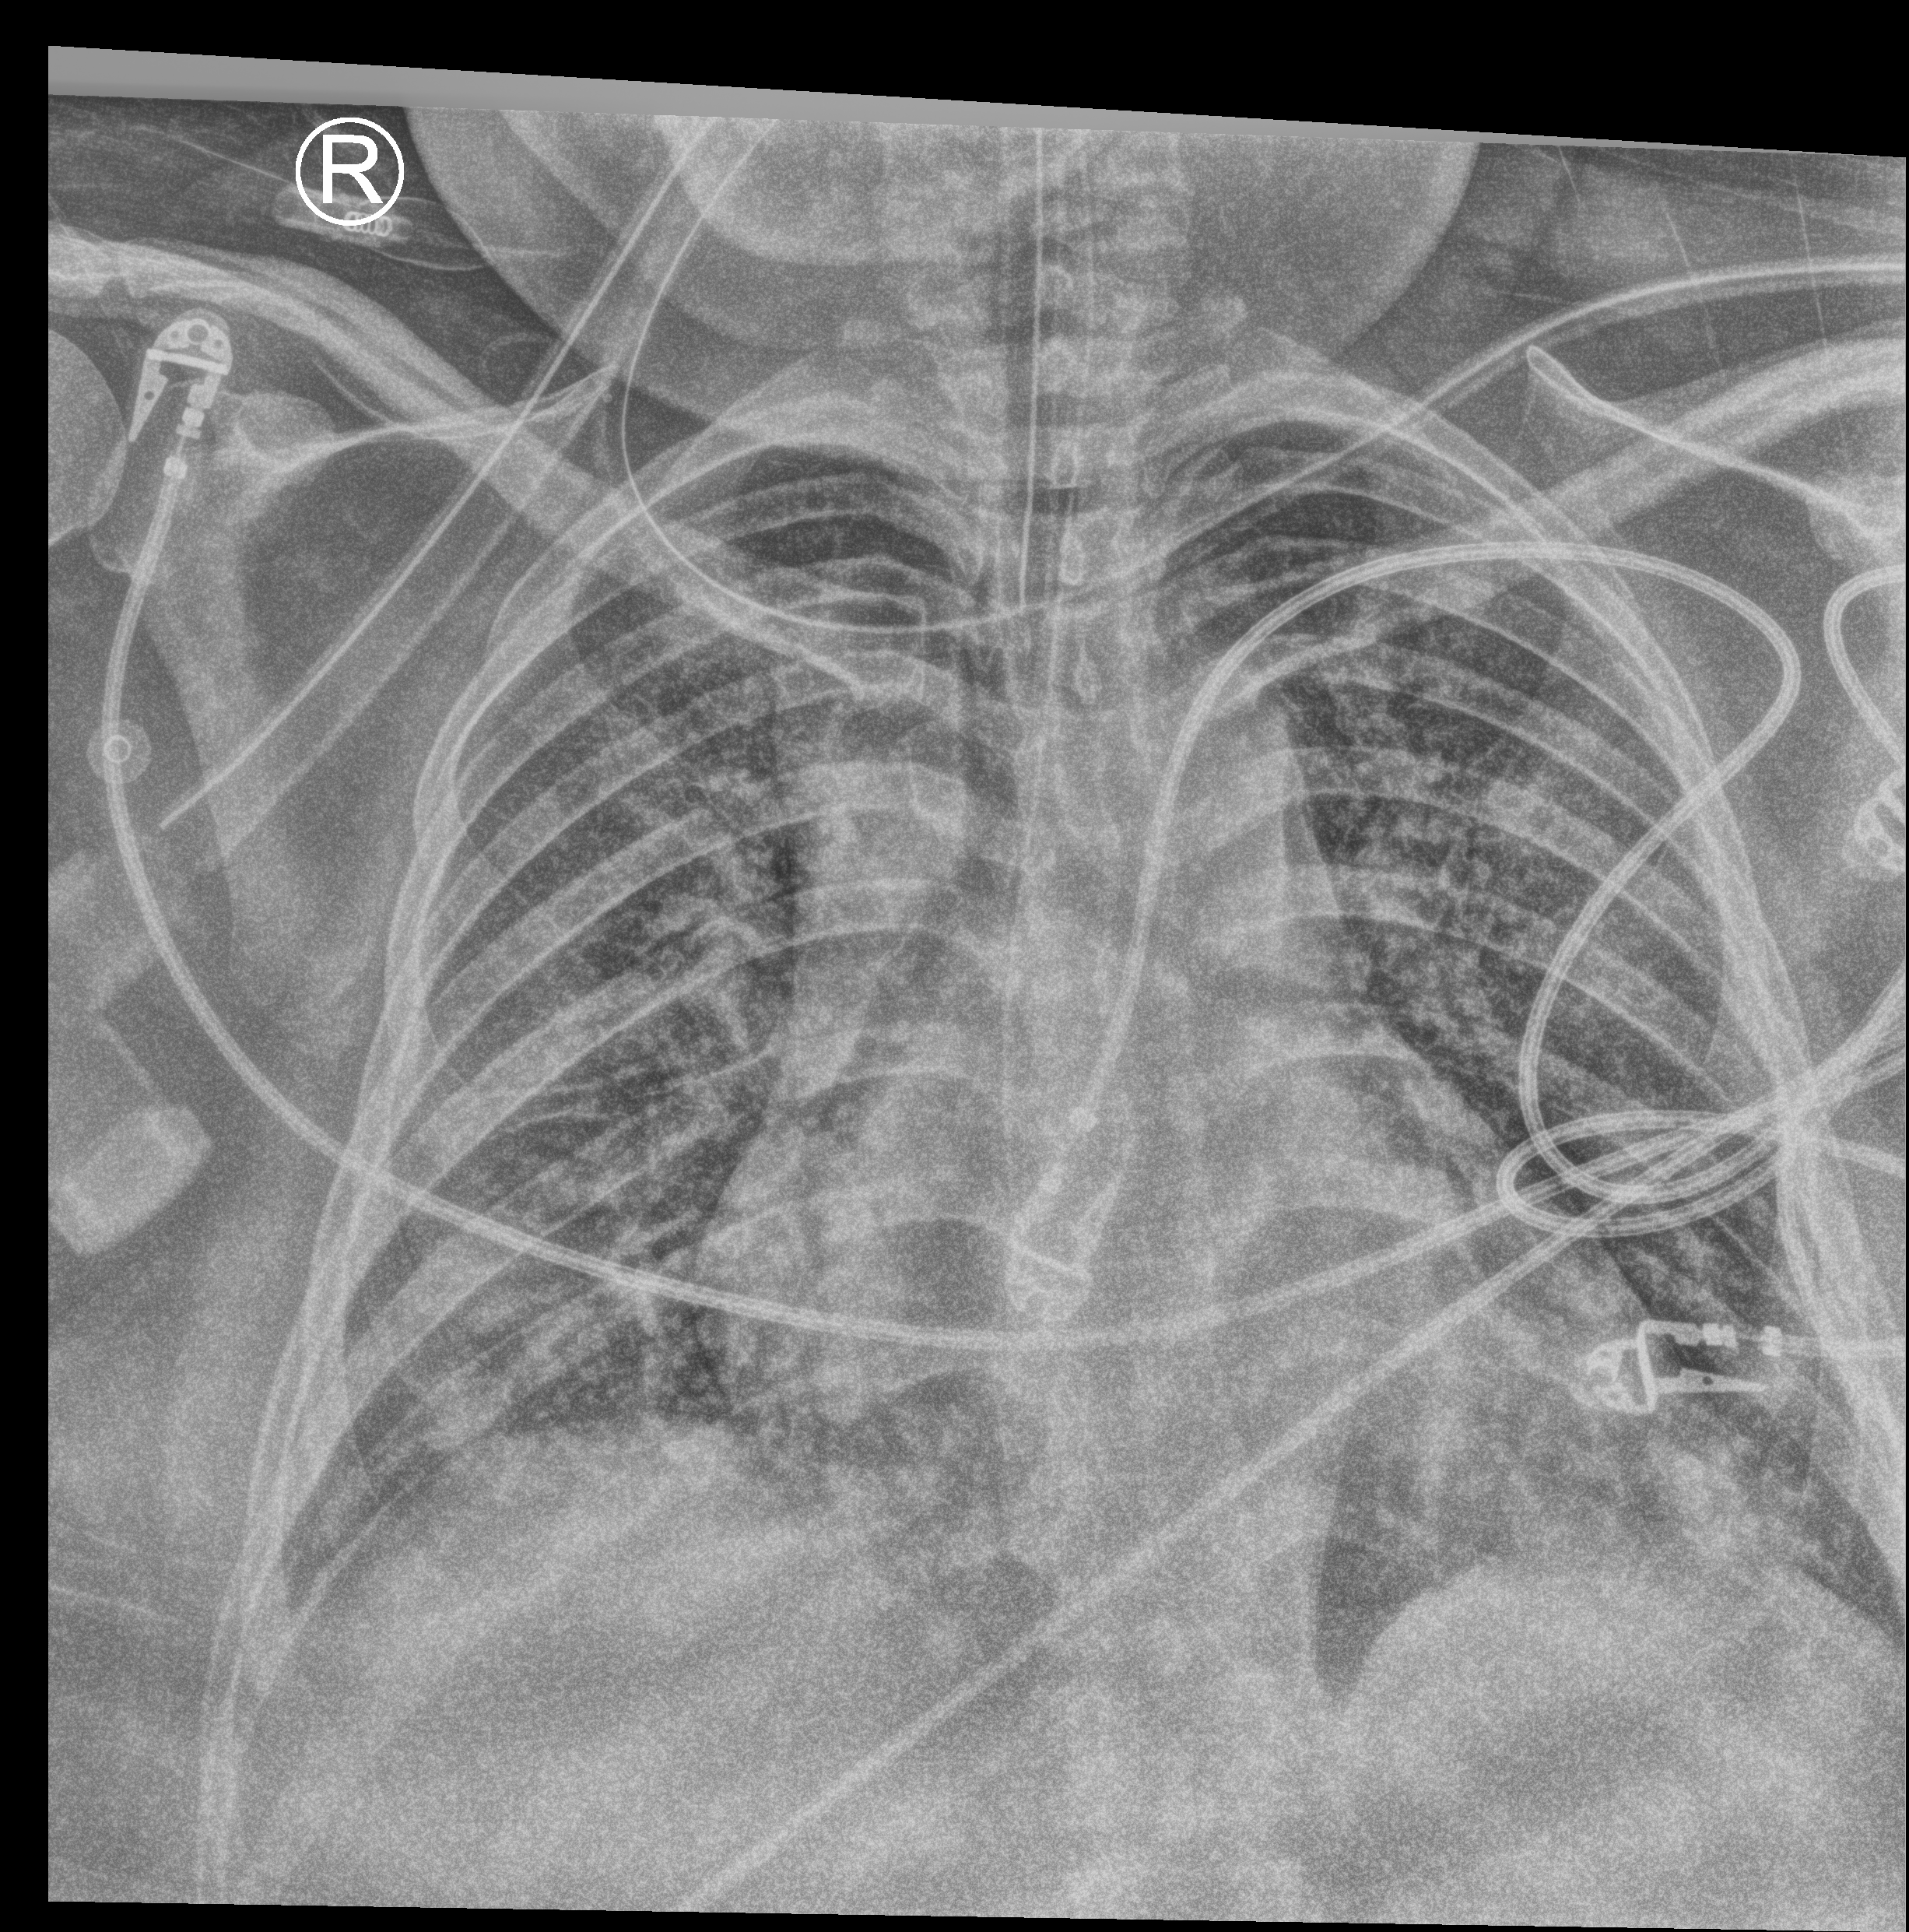
Chest X-ray (portable); anteroposterior (AP) projection. Female patient hospitalised with COVID-19, age 18–59 years.
Admission-level facts for this patient (not findings on this image; timing relative to this image not recorded): mechanically ventilated during this hospital stay: yes.